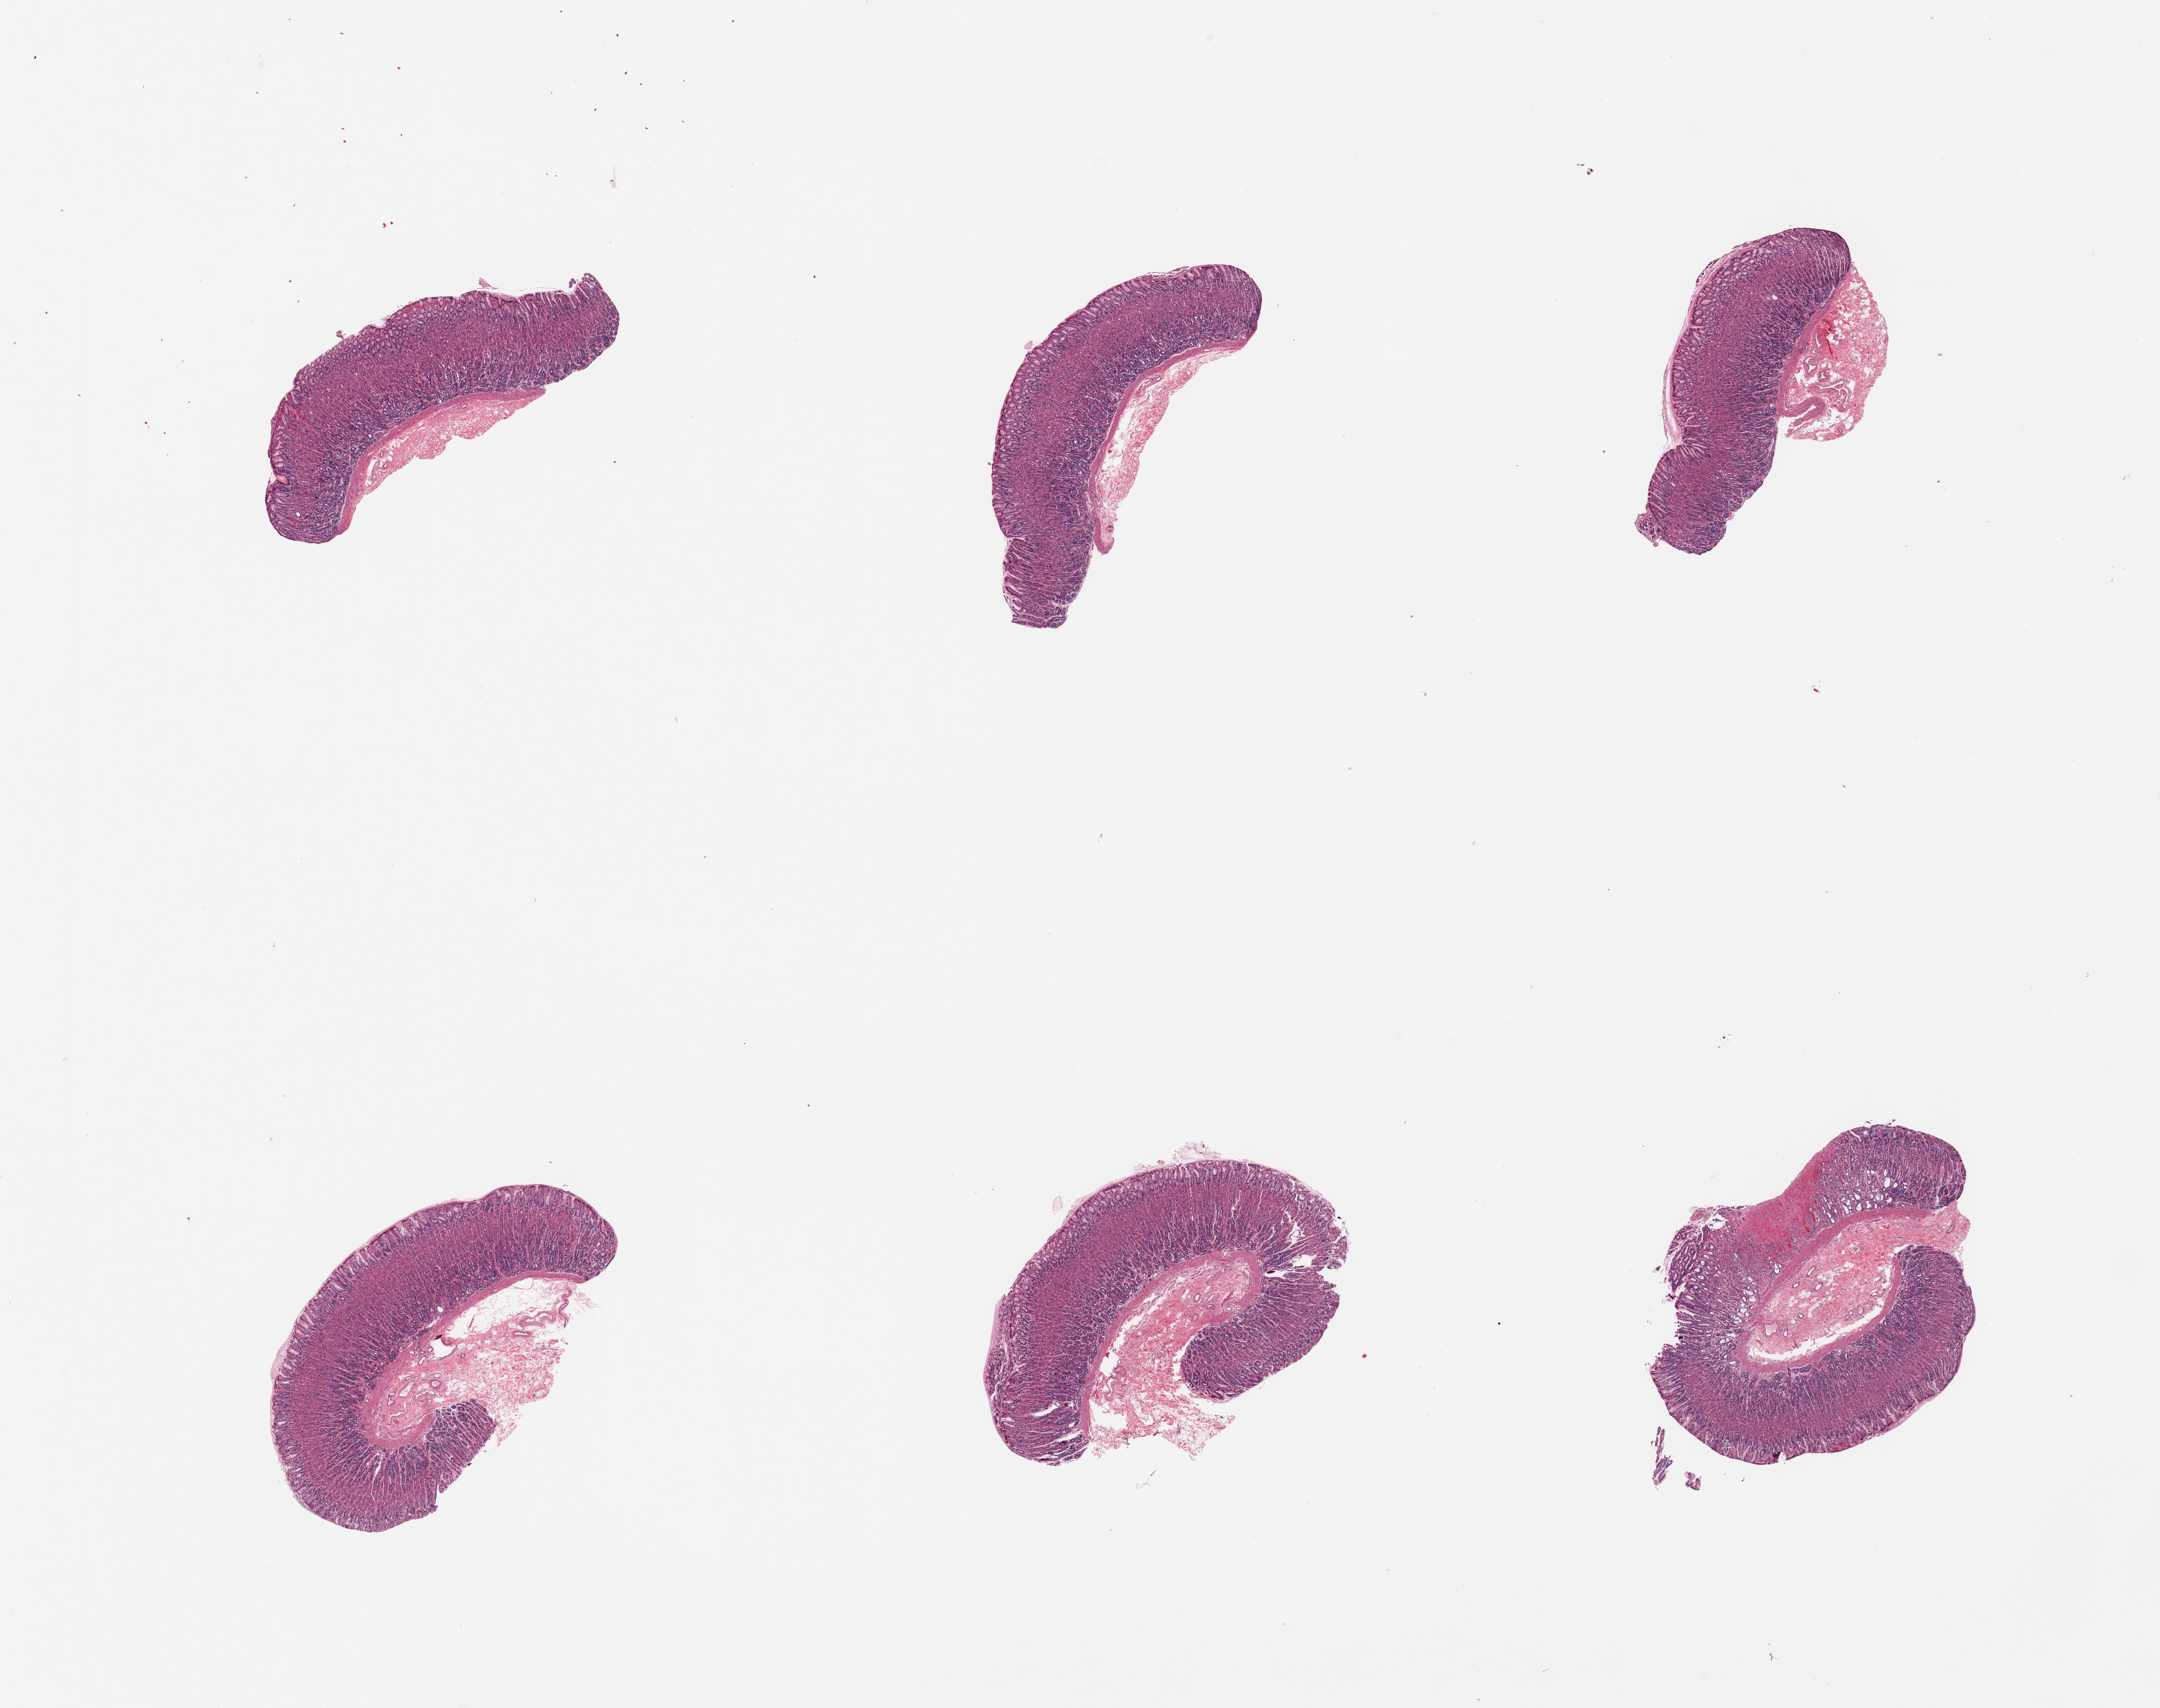
Digitized H&E-stained section — a low-resolution overview of the entire scanned area, about 24.6 x 19.5 mm. PAXgene-fixed paraffin-embedded (PFPE) section. Sampled site (target tissue): stomach. Tissue donor sample. Donor sex: male.
Reviewer comment on this tissue sample: 6 pieces, mucosa ~80-100% thickness, well-preserved.